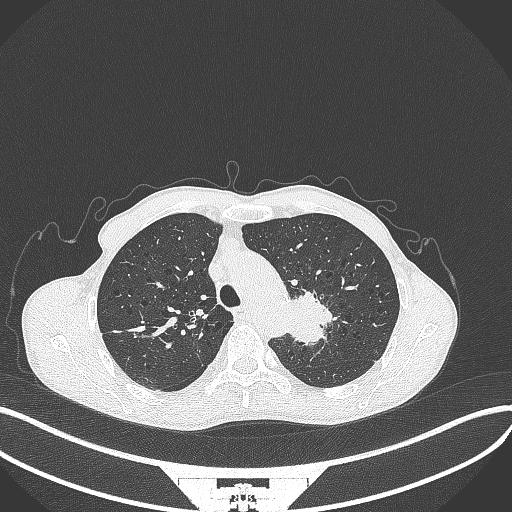
Chest CT, one axial slice. Position 316 of 386 along the scan axis. 120 kVp. Lung window (W 1500 / L -600 HU). 1 mm slice thickness. 512 × 512 image matrix. Male patient, age 65 years. From the clinical record (not read from this slice): clinical TNM (as recorded): T2b N0 M0.
Annotated regions visible in this slice (rectangle marked by the reading radiologist):
- lung tumour (recorded histology: adenocarcinoma): bounding box [x1, y1, x2, y2] px = [287, 282, 341, 353]